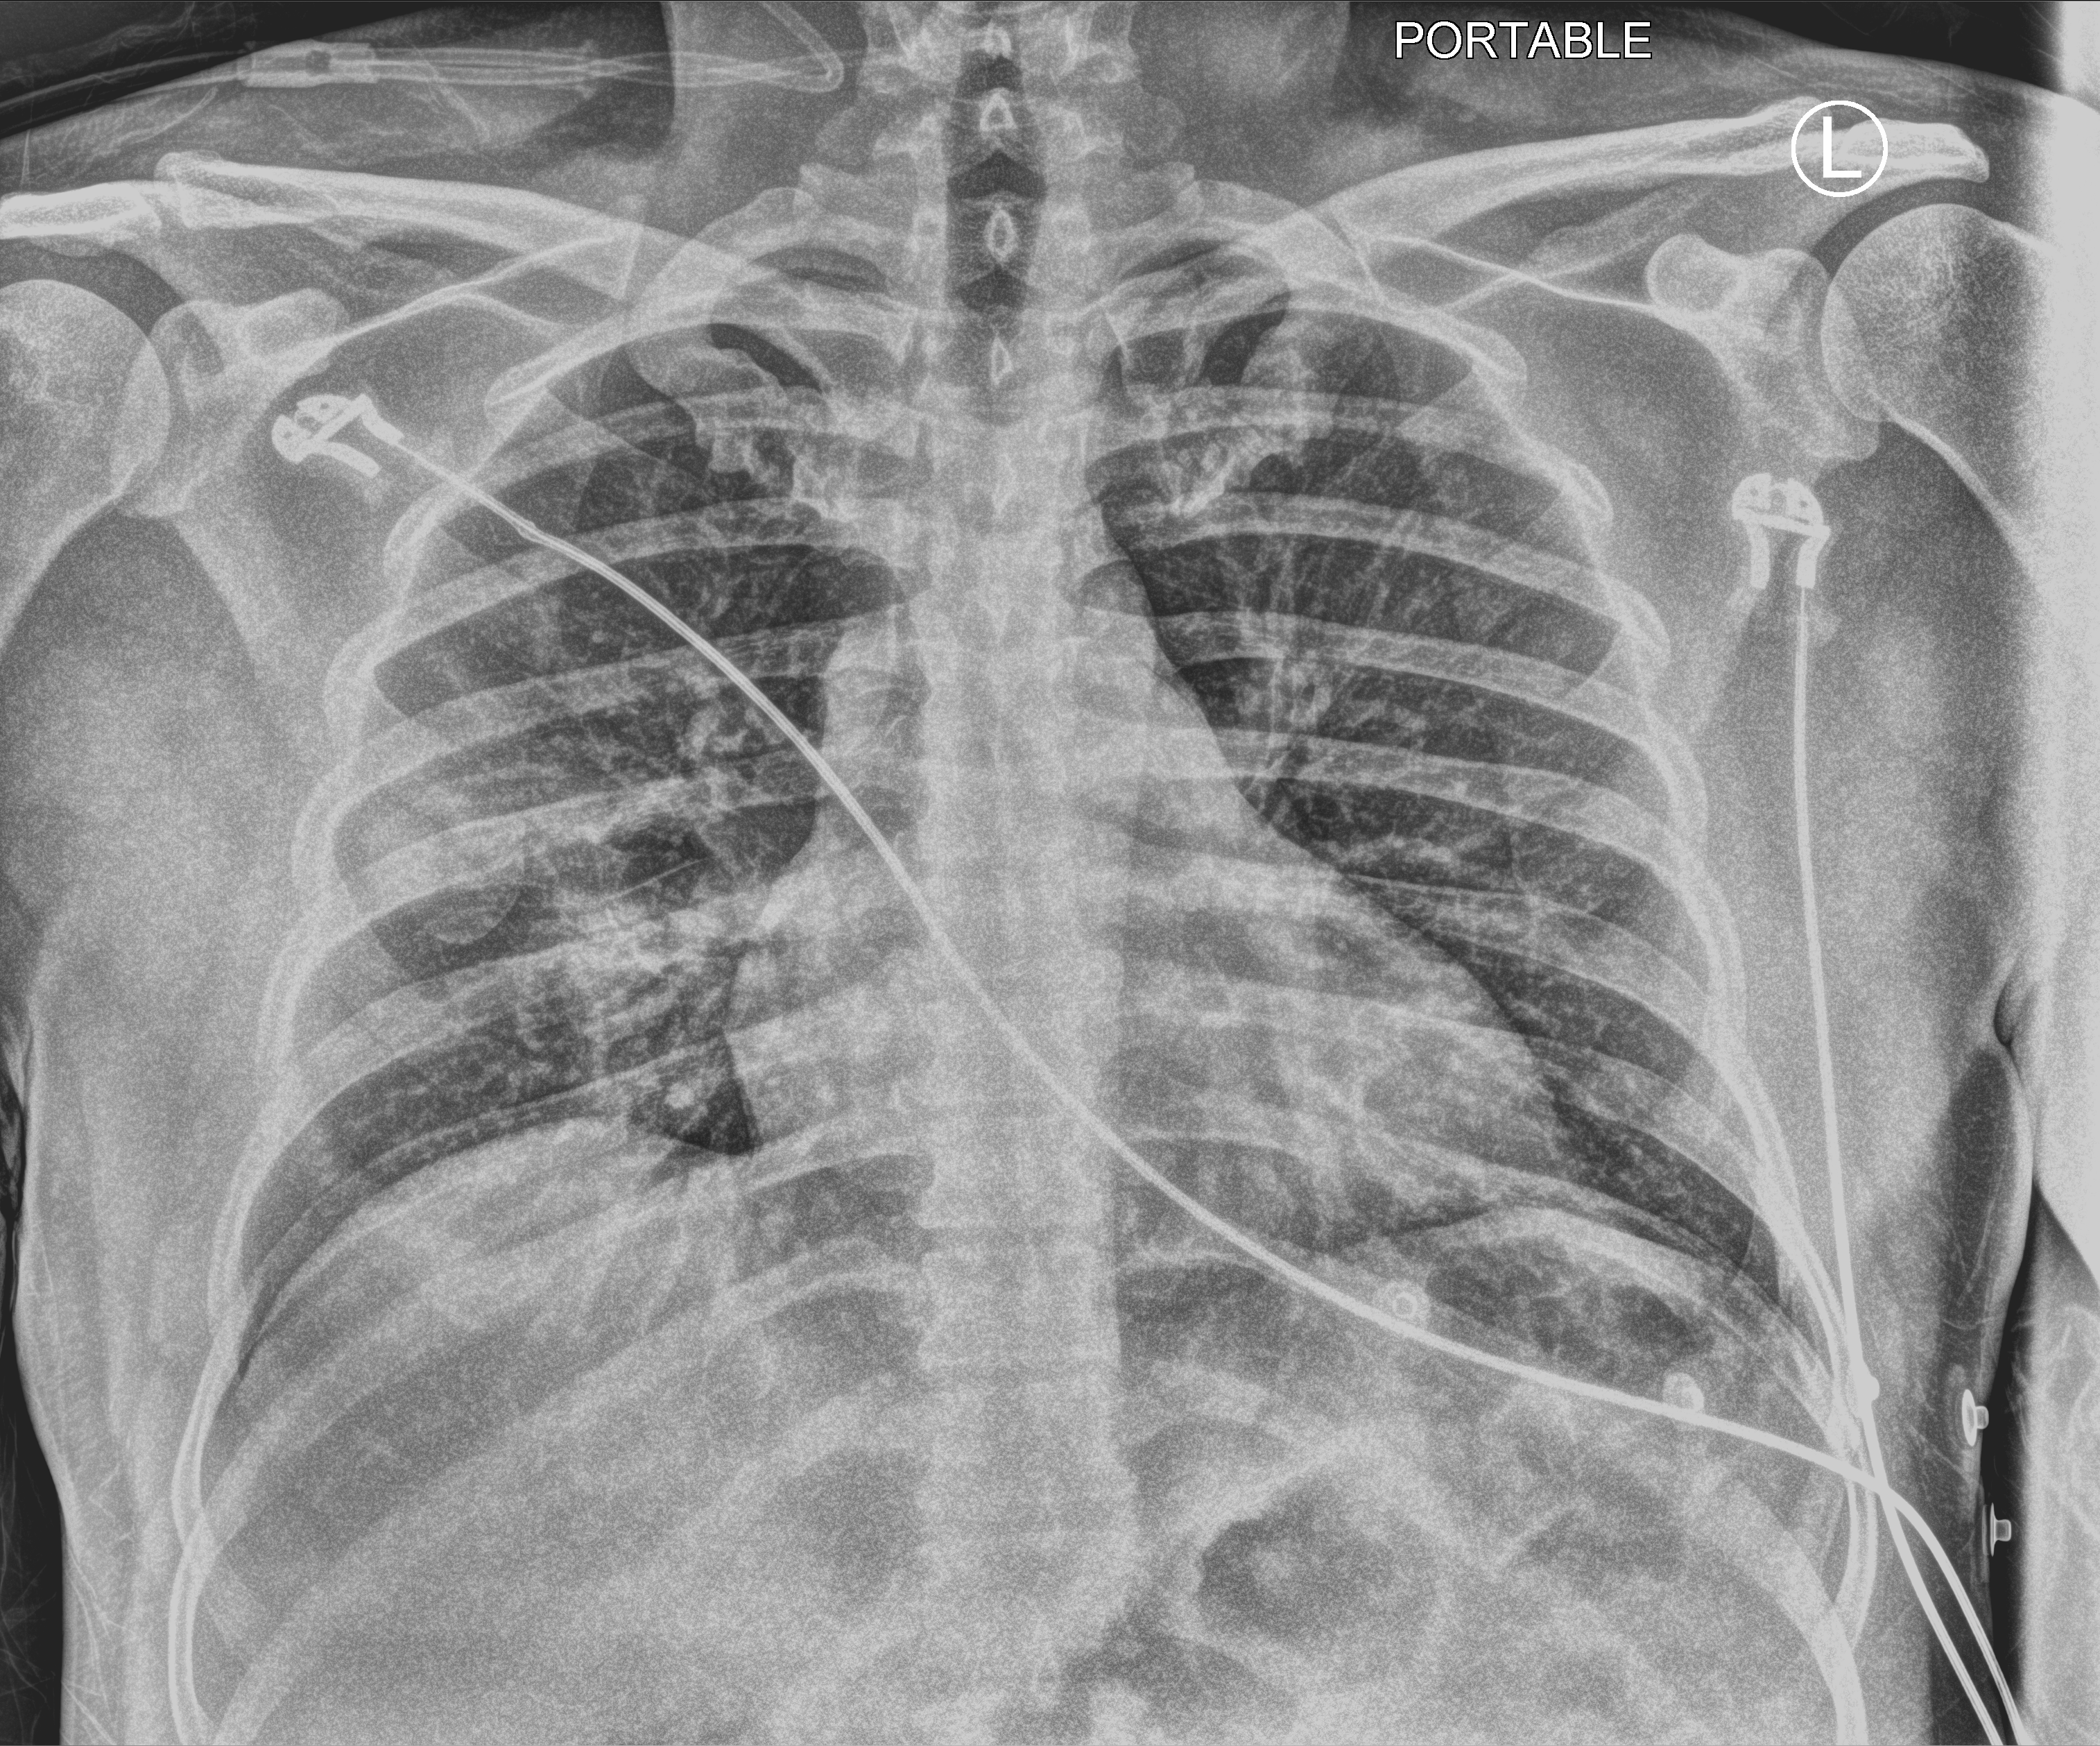
Chest X-ray (portable); anteroposterior (AP) projection. Patient hospitalised with COVID-19; male, aged 18–59 years.
From the hospital-stay record, not from the radiograph (when in the stay this image was taken is not recorded):
- chronic kidney disease (admission record): no
- length of hospital stay: 10 days